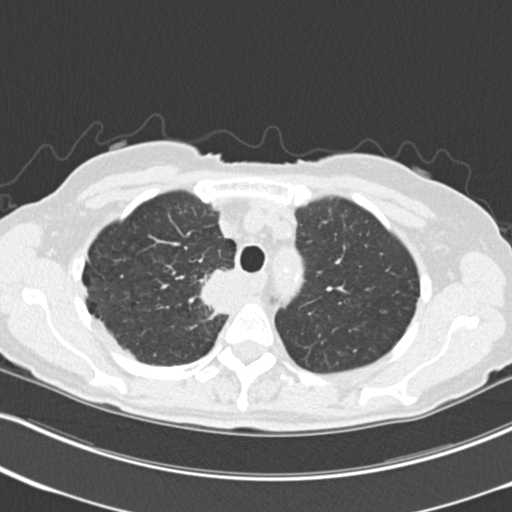
Low-dose screening chest CT, axial slice; third screening round (two years after baseline); lung window (W 1500 / L -600 HU); 2 mm slice thickness; 120 kVp; slice 50 of 226 in the series; 512 × 512 image matrix. Female participant, aged 68 years at enrolment. Current smoker at enrolment.
Expert-annotated lung lesion, bounding box <198,265,250,320> (left, top, right, bottom; pixels). Reader record for this screening exam (exam-level; its link to the box is not recorded): non-calcified nodule or mass ≥4 mm, right upper lobe, 31 × 29 mm, poorly defined margins, soft tissue attenuation, pre-existing on the prior screen: no. Official screen result: positive, other. Participant outcome: lung cancer diagnosed 79 days after this screen — squamous cell carcinoma, NOS, right upper lobe, mediastinum, poorly differentiated (G3), stage IIIB (AJCC 6th edition), 43 mm at pathology.